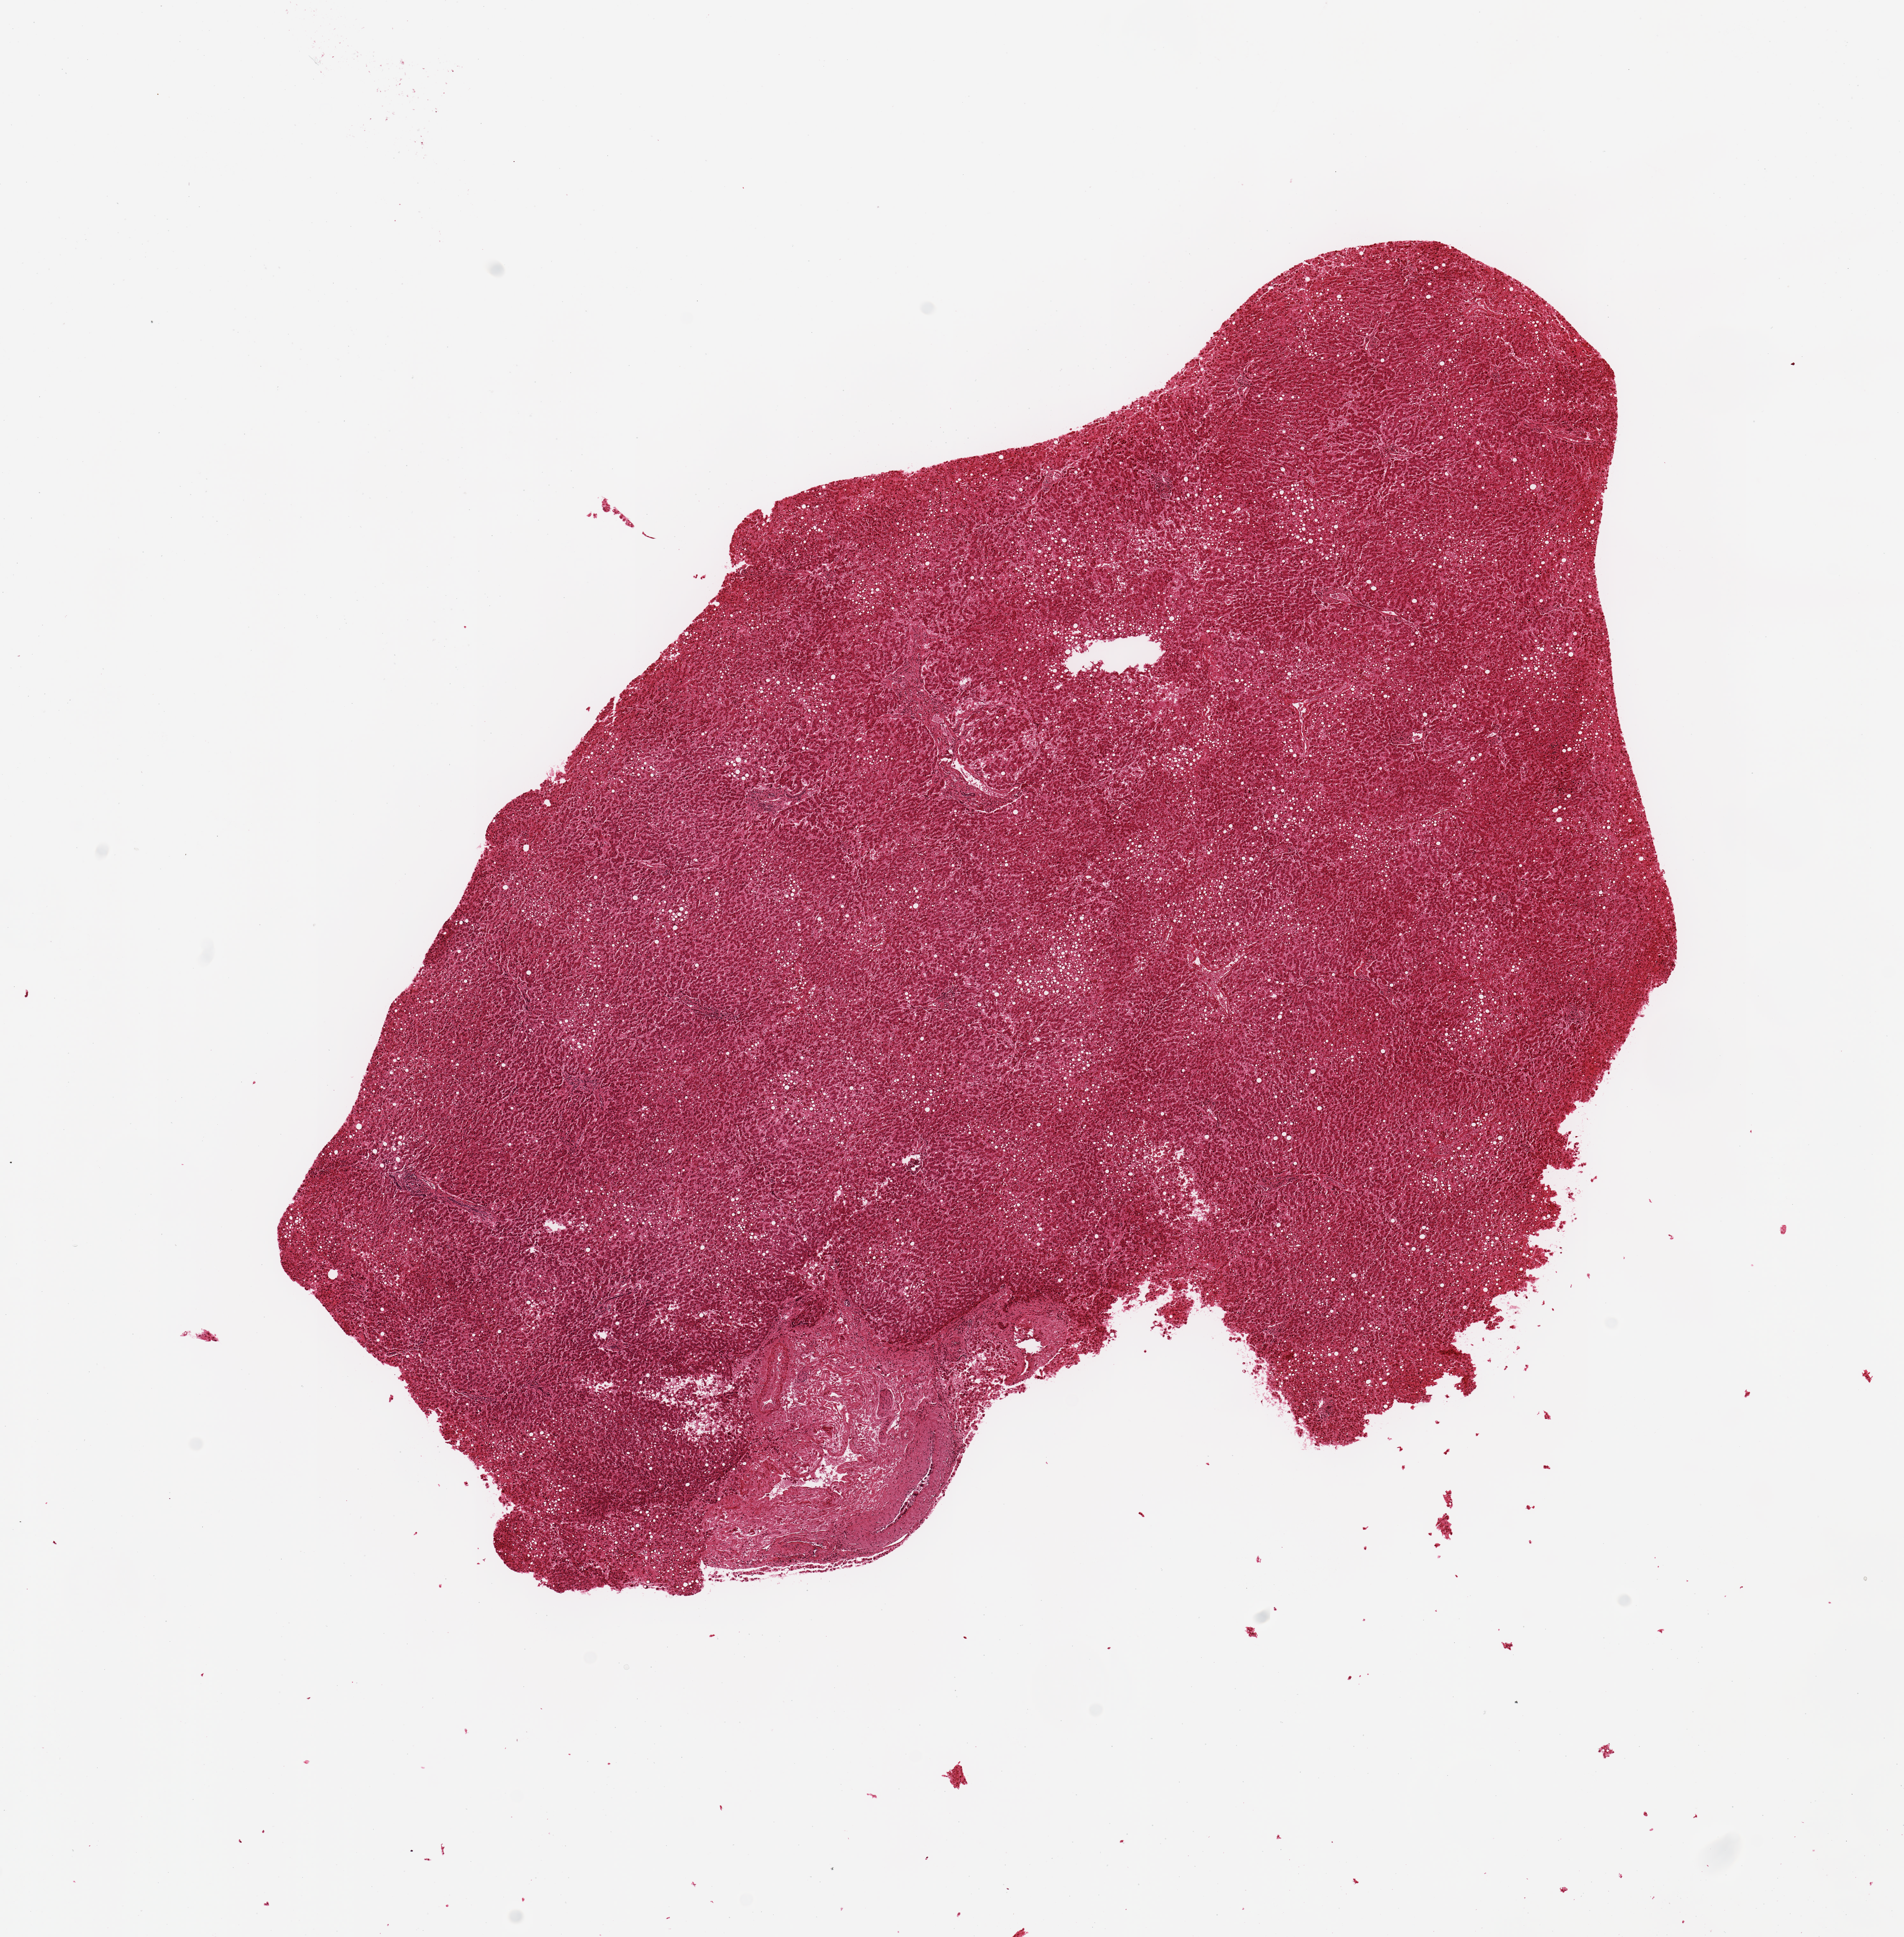
Digitized H&E-stained section, brightfield — shown as a low-resolution overview of the whole scanned area (about 11.8 x 12.0 mm, acquisition: 20x scan). PAXgene-fixed paraffin-embedded (PFPE) section. Section of liver (target tissue). Tissue donor sample. Donor: female.
Review note (as recorded): 9.7x6.7mm. Patchy macrovesicular steatosis, 3-40%. Focal central areas appear under-fixed with tears/holes.